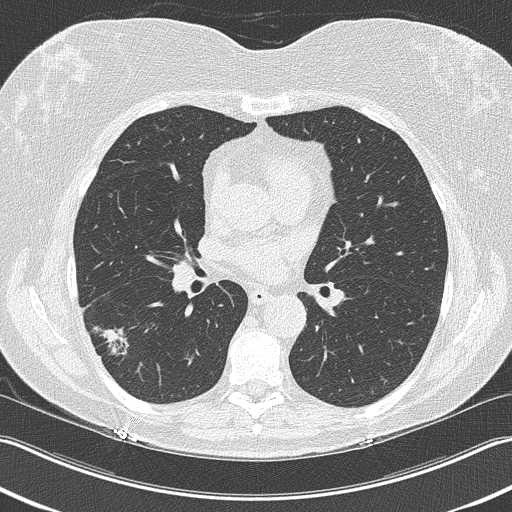
Low-dose screening chest CT, one axial slice; position 120 of 210 along the scan axis; reconstruction kernel B50f; 120 kVp; lung window (W 1500 / L -600 HU); 512 × 512 image matrix, field of view 348 × 348 mm.
Annotated regions visible in this slice (expert manual segmentation):
- lesion 1 (tumor, lower lobe of right lung): bounding box <92,326,130,356> (left, top, right, bottom; pixels)